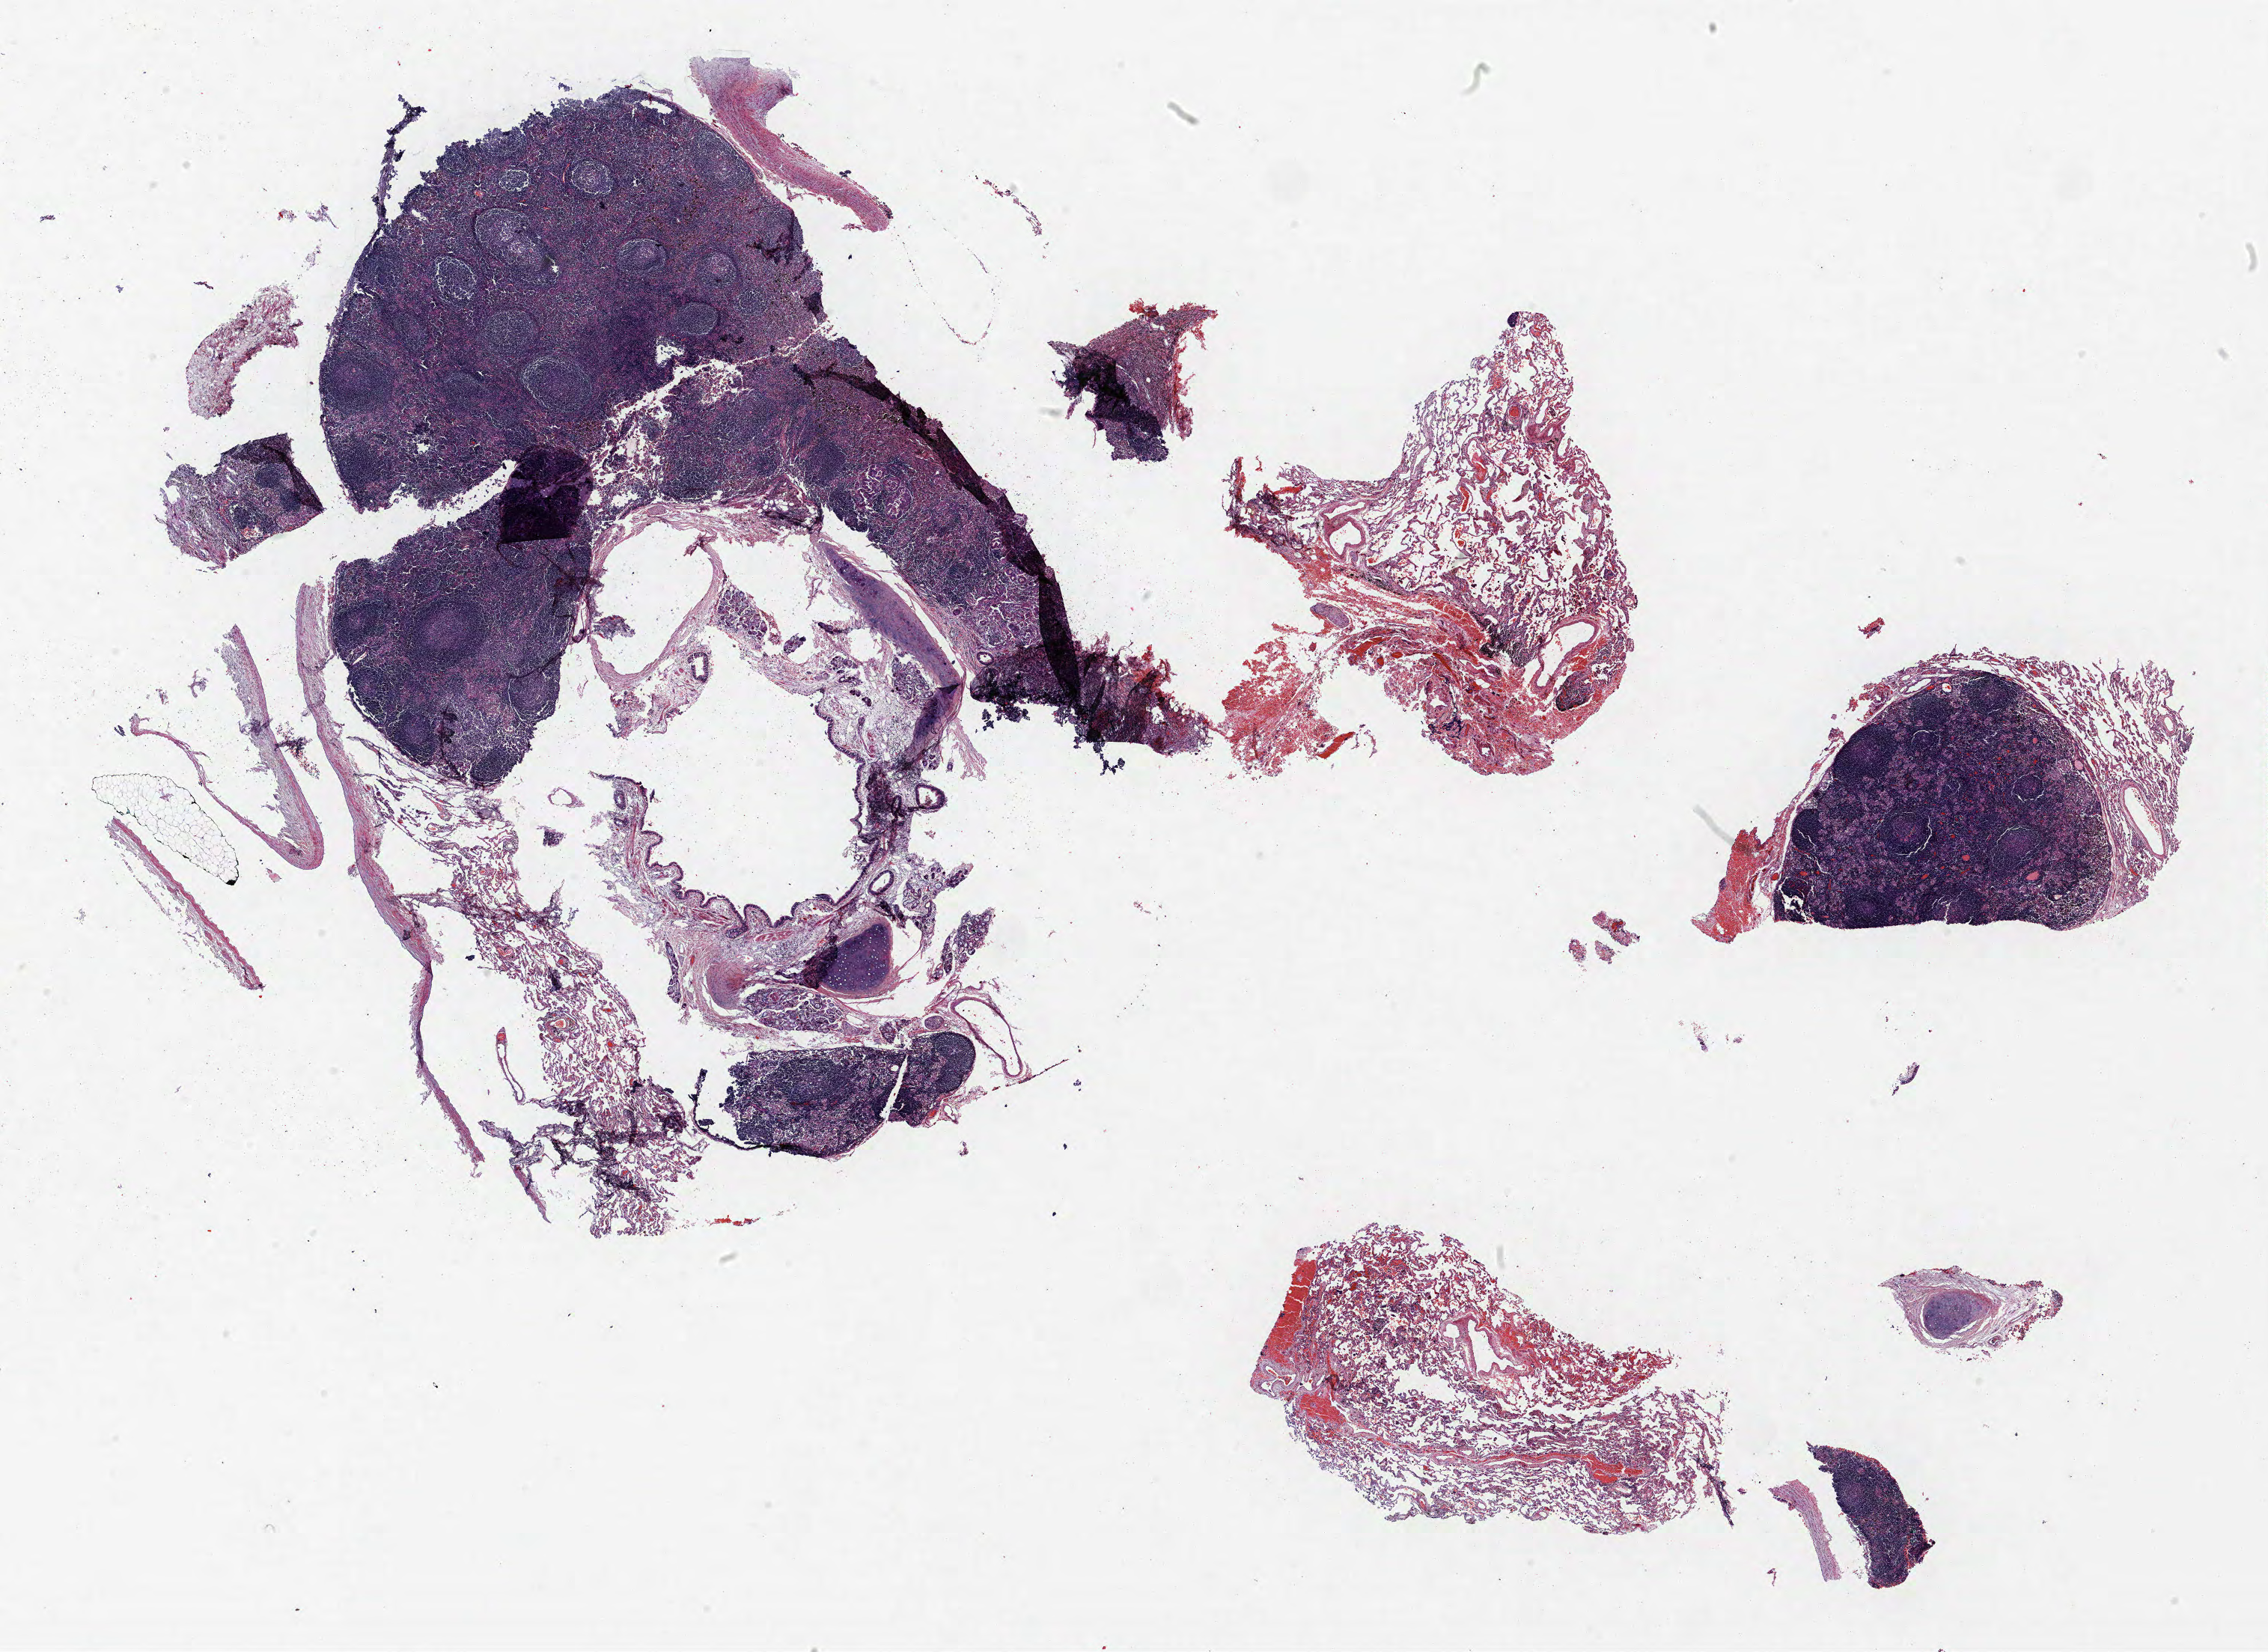
H&E whole-slide image — low-resolution overview of the scanned area, about 24.2 x 17.7 mm (slide scanned at 40x); FFPE section; lung tissue. Female patient, aged 61 at enrolment. Current smoker at enrolment. Grade: well differentiated (G1).
• participant's lung-cancer diagnosis: Adenocarcinoma, NOS (ICD-O-3 8140/3)
• primary tumour location (clinical record): right upper lobe
• stage (AJCC 6th edition): IIIB
• tumour size (pathology): 30 mm
• ICD-O-3 topography: upper lobe of lung (C34.1)
• note: participant had 2 primary lung cancers recorded; fields above describe the first